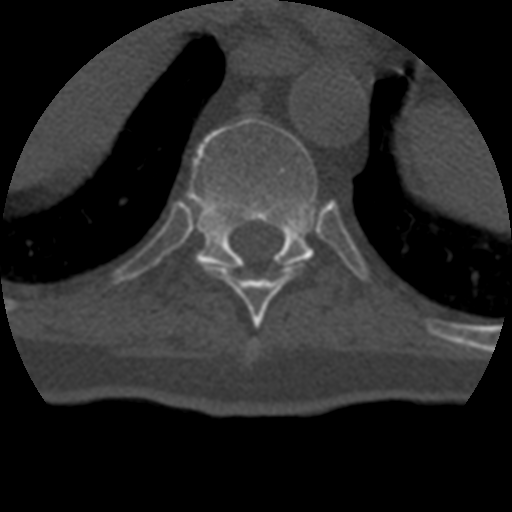
CT including the spine, one axial slice; position 229 of 399 along the scan axis; 120 kVp; bone window (W 1800 / L 400 HU); 512 × 512 image matrix. Patient age 69 years. Case-level facts recorded for this patient, not image findings: primary cancer: prostate.
Annotated regions visible in this slice (semi-automatic segmentation, software-assisted and operator-edited):
- T10 vertebra: bounding box [x1, y1, x2, y2] px = [188, 118, 317, 268]
- T9 vertebra: [208, 261, 307, 321]